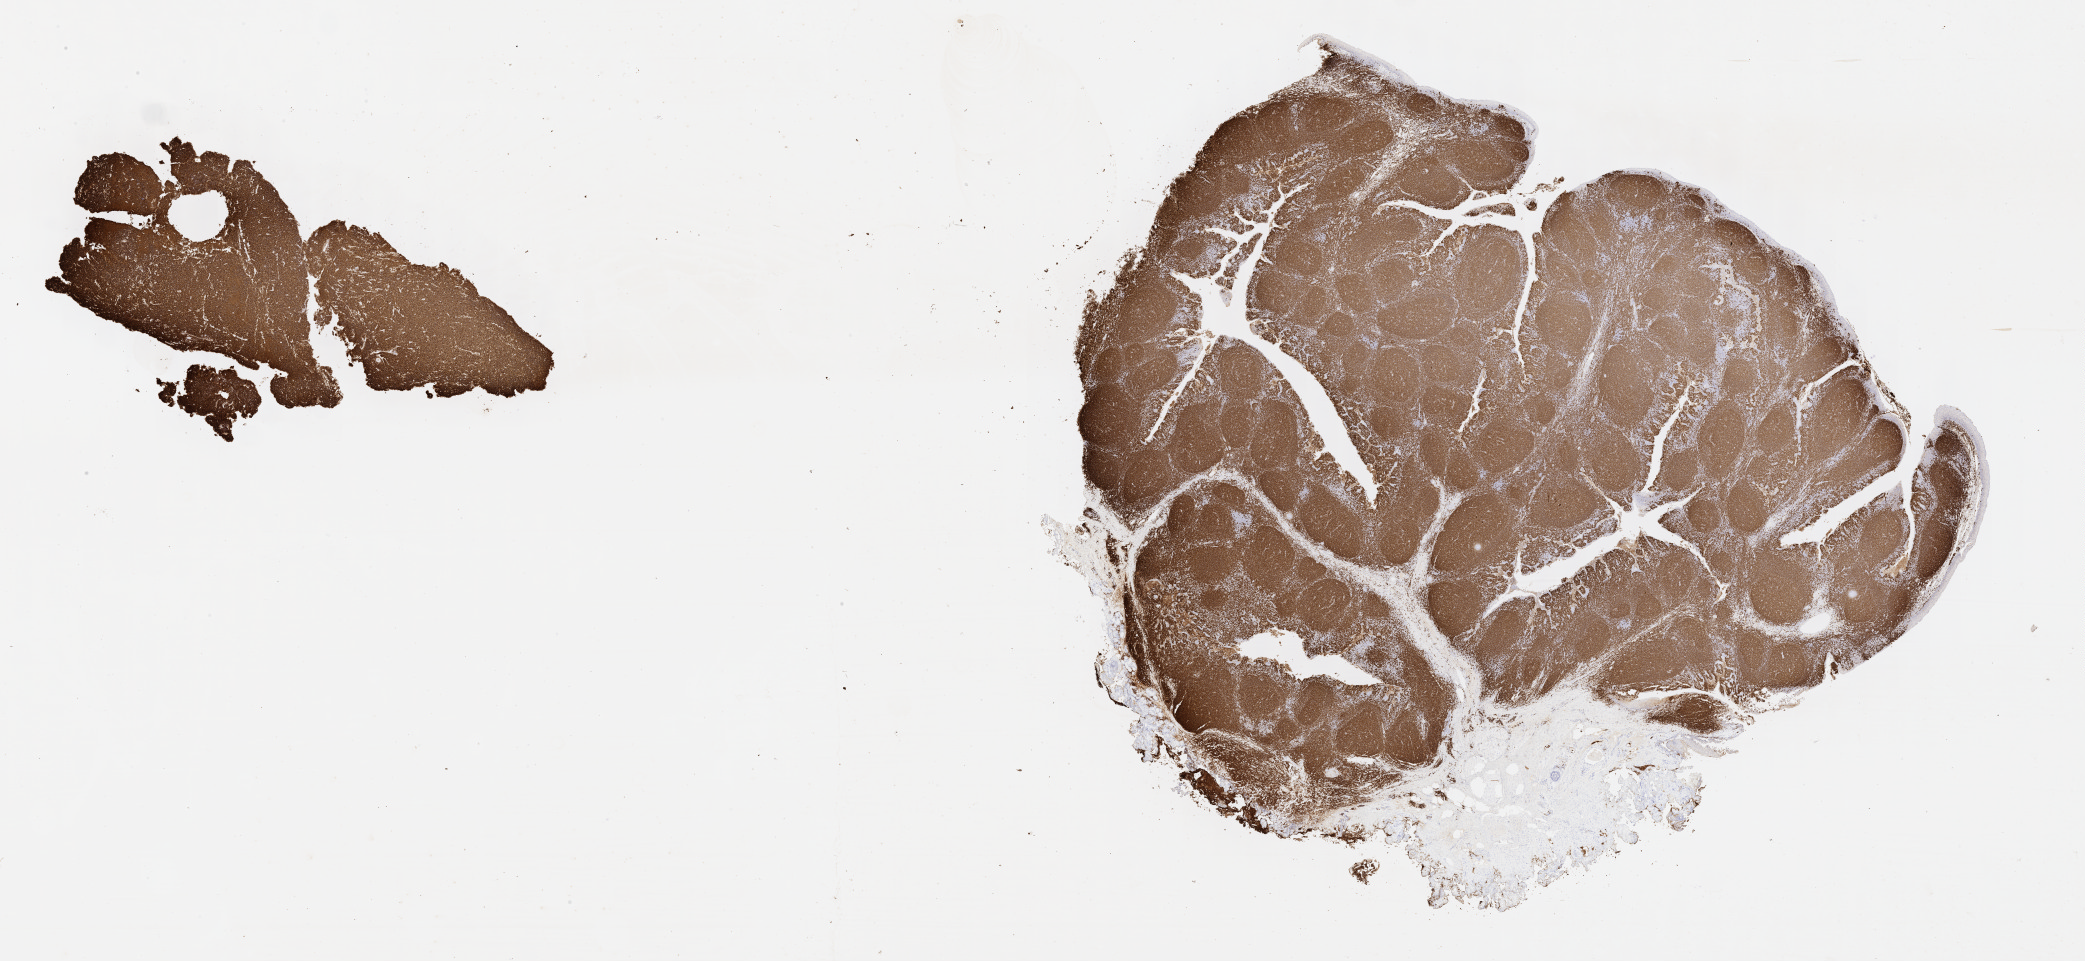
Immunohistochemistry (IHC) whole-slide image stained for CD20, whole scanned area (about 33.7 x 15.5 mm) shown as a low-resolution overview; tumor tissue; site: mandible. Patient male; age 25 years.
• diagnosis: Diffuse large B-cell lymphoma, NOS